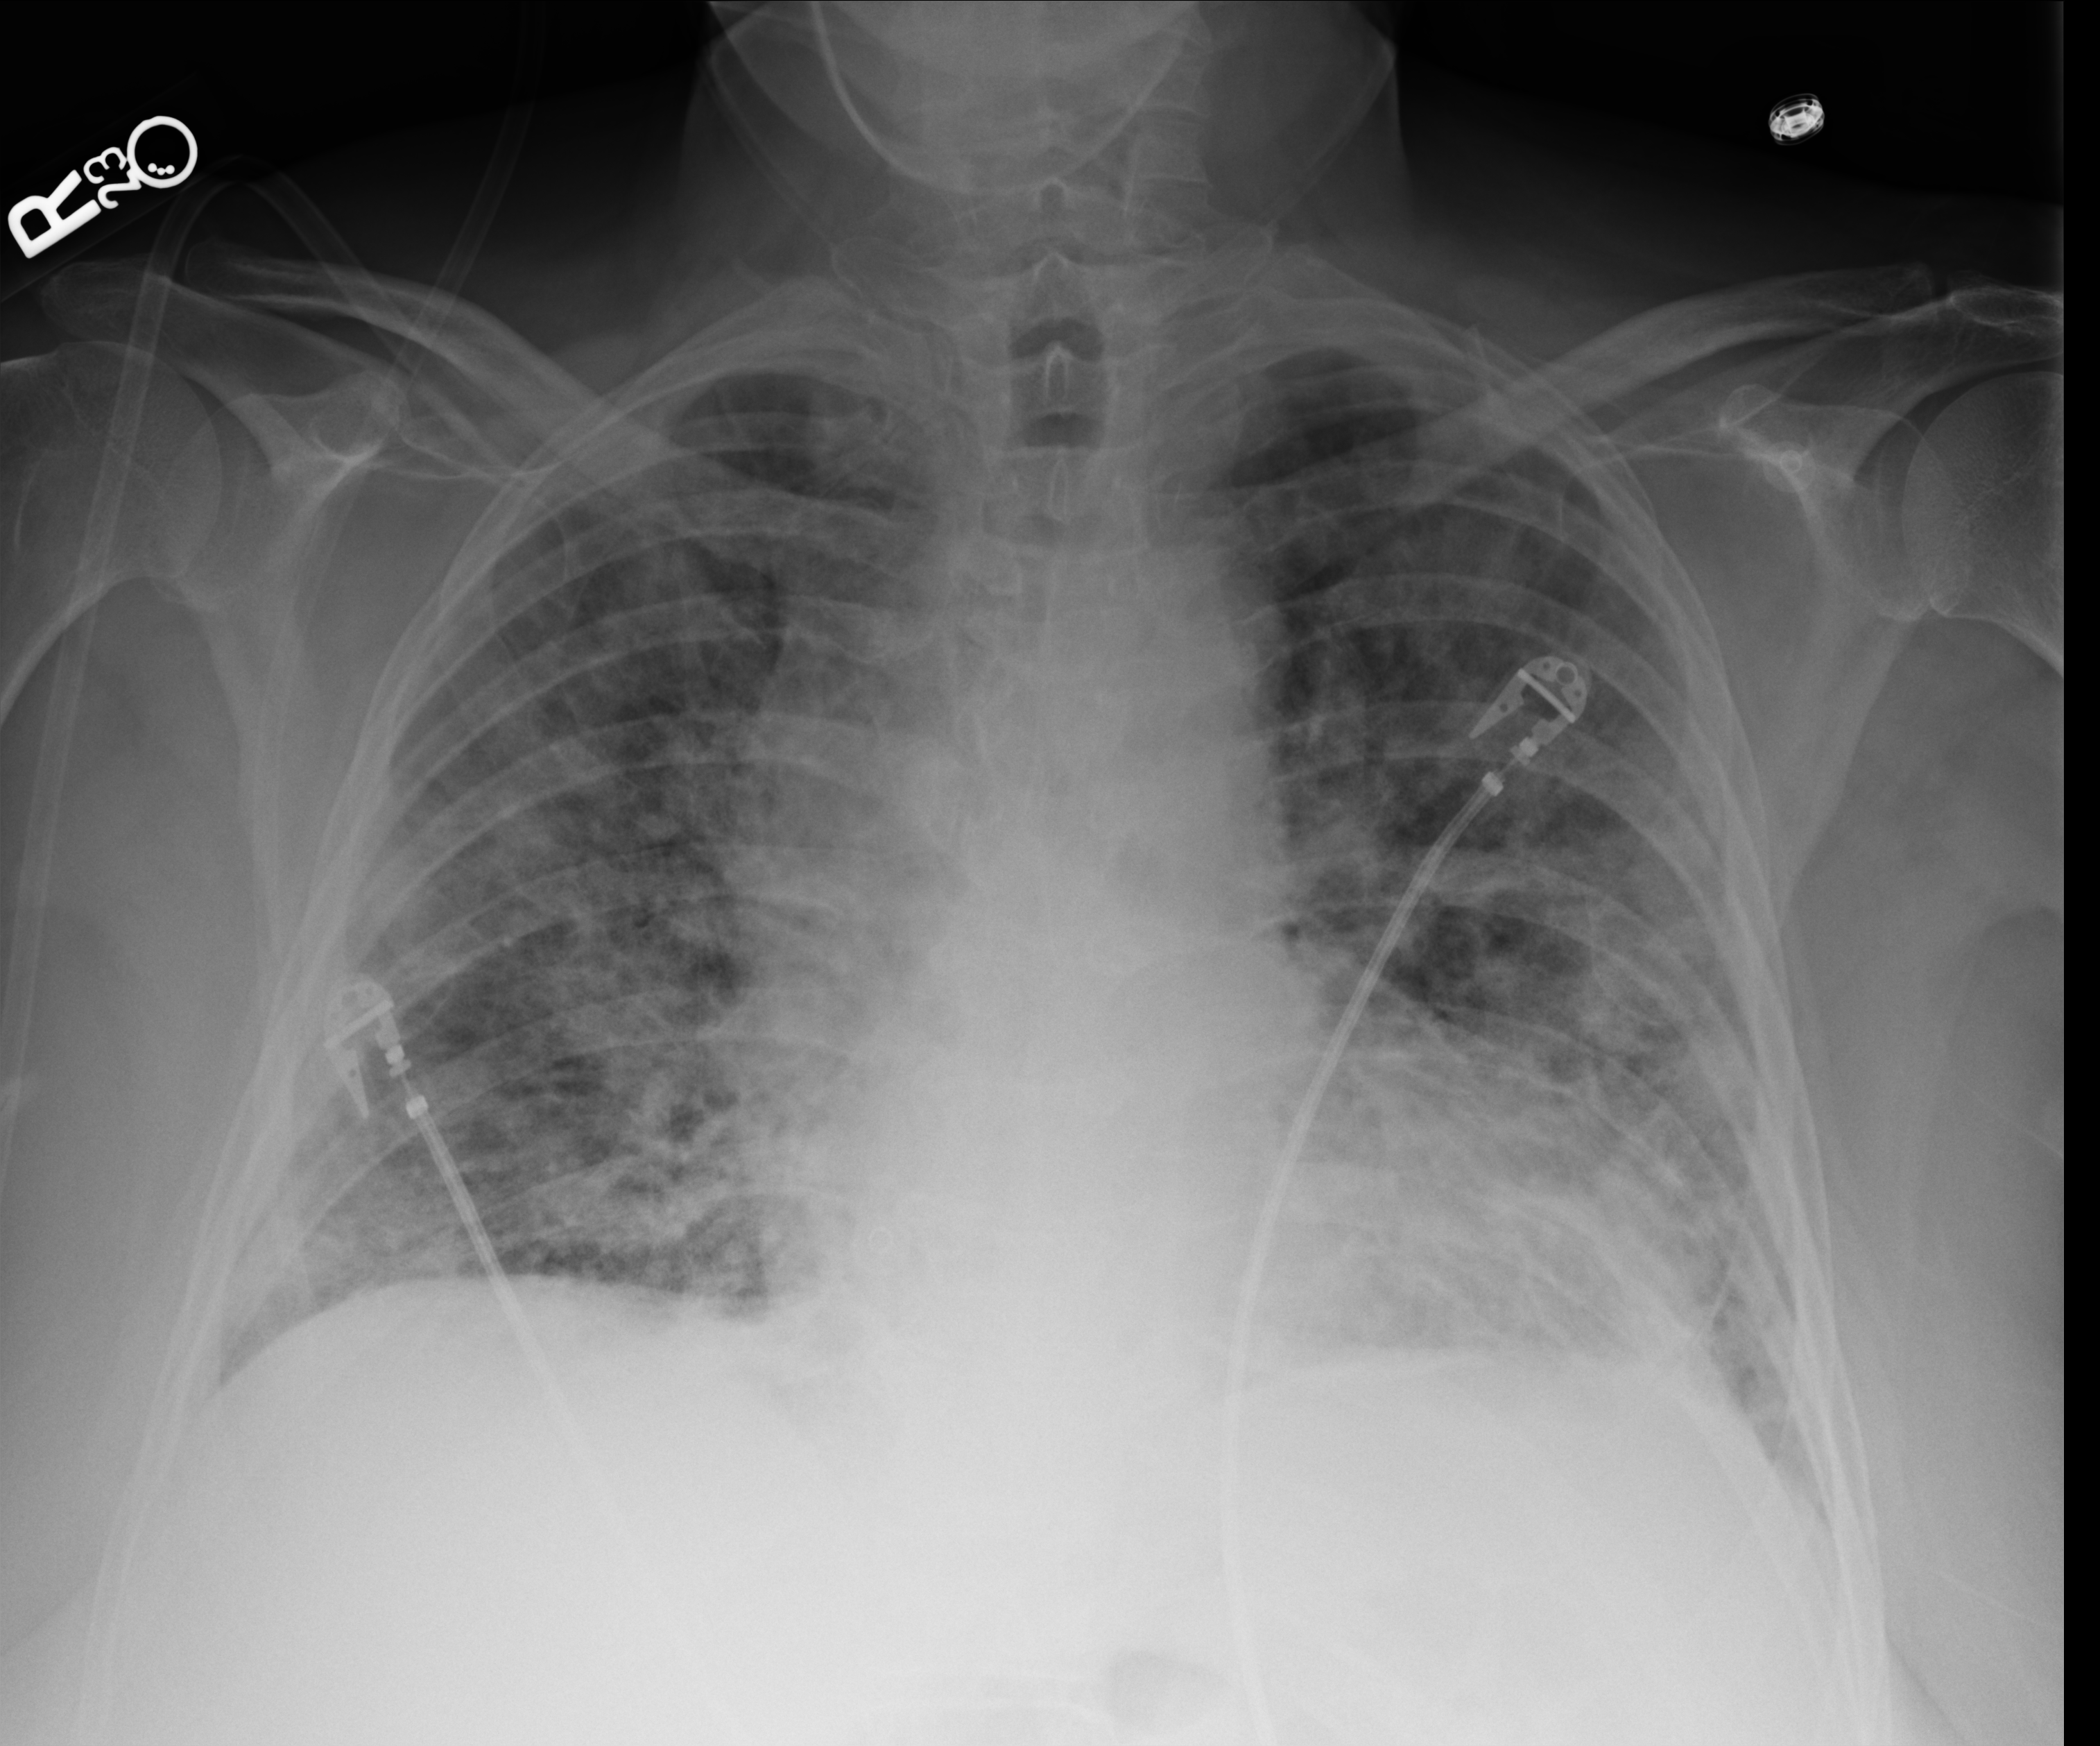
Bedside chest radiograph (computed radiography), anteroposterior (AP) projection. Female patient hospitalised with COVID-19, age 60–74 years.
Hospital-stay facts (about this admission, not read from this image; timing relative to this image not recorded): mechanically ventilated during this hospital stay: no; COPD (admission record): no.